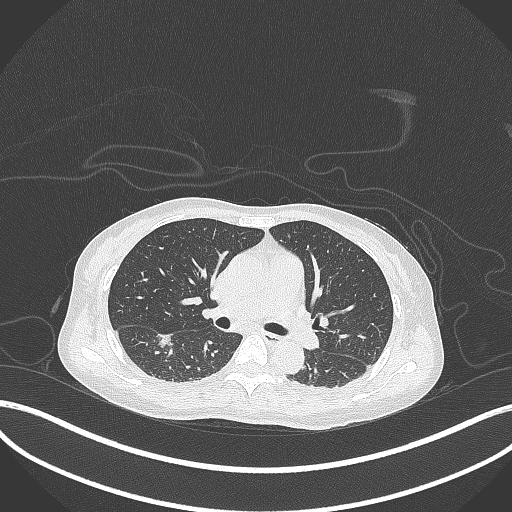
Chest CT, one axial slice; slice 182 of 261 in the series (ordered by position); reconstruction kernel B70f; 120 kVp; lung window (W 1500 / L -600 HU); 1 mm slice thickness; 512 × 512 image matrix, field of view 400 × 400 mm. Patient: female, 44 years. Case-level facts recorded for this patient, not image findings: clinical TNM (as recorded): T1c N0 M0.
Annotated regions visible in this slice (bounding box drawn by a radiologist):
- lung tumour (recorded histology: adenocarcinoma): bounding box (x1, y1, x2, y2) in pixels: (155, 331, 177, 350)